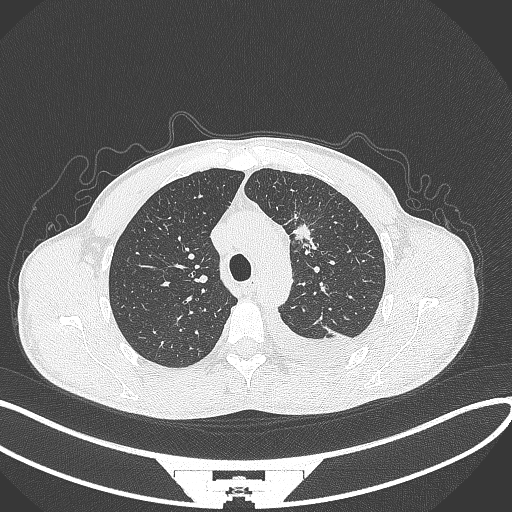
Chest CT, one axial slice. Slice 245 of 371 in the series (ordered by position). Reconstruction kernel B70f. 120 kVp. Lung window (W 1500 / L -600 HU). 1 mm slice thickness. 512 × 512 image matrix. Male patient, age 49 years. From the clinical record (not read from this slice): clinical TNM (as recorded): T1c N1 M1.
Structures marked on this image (bounding box drawn by a radiologist):
- lung tumour (recorded histology: adenocarcinoma): bounding box (x1, y1, x2, y2) in pixels: (288, 209, 315, 250)